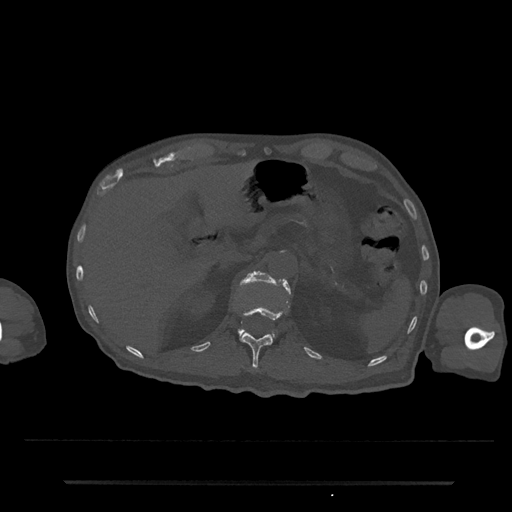
CT including the spine, one axial slice; position 176 of 797 along the scan axis; 120 kVp; bone window (W 1800 / L 400 HU); 0.5 mm slice thickness; 512 × 512 image matrix, field of view 427 × 427 mm. Male patient, age 74 years. Case-level facts recorded for this patient, not image findings: primary cancer: prostate.
Outlined on this slice (semi-automatic segmentation, software-assisted and operator-edited):
- L1 vertebra: bounding box [x1, y1, x2, y2] px = [239, 271, 291, 337]
- T12 vertebra: [241, 307, 288, 371]